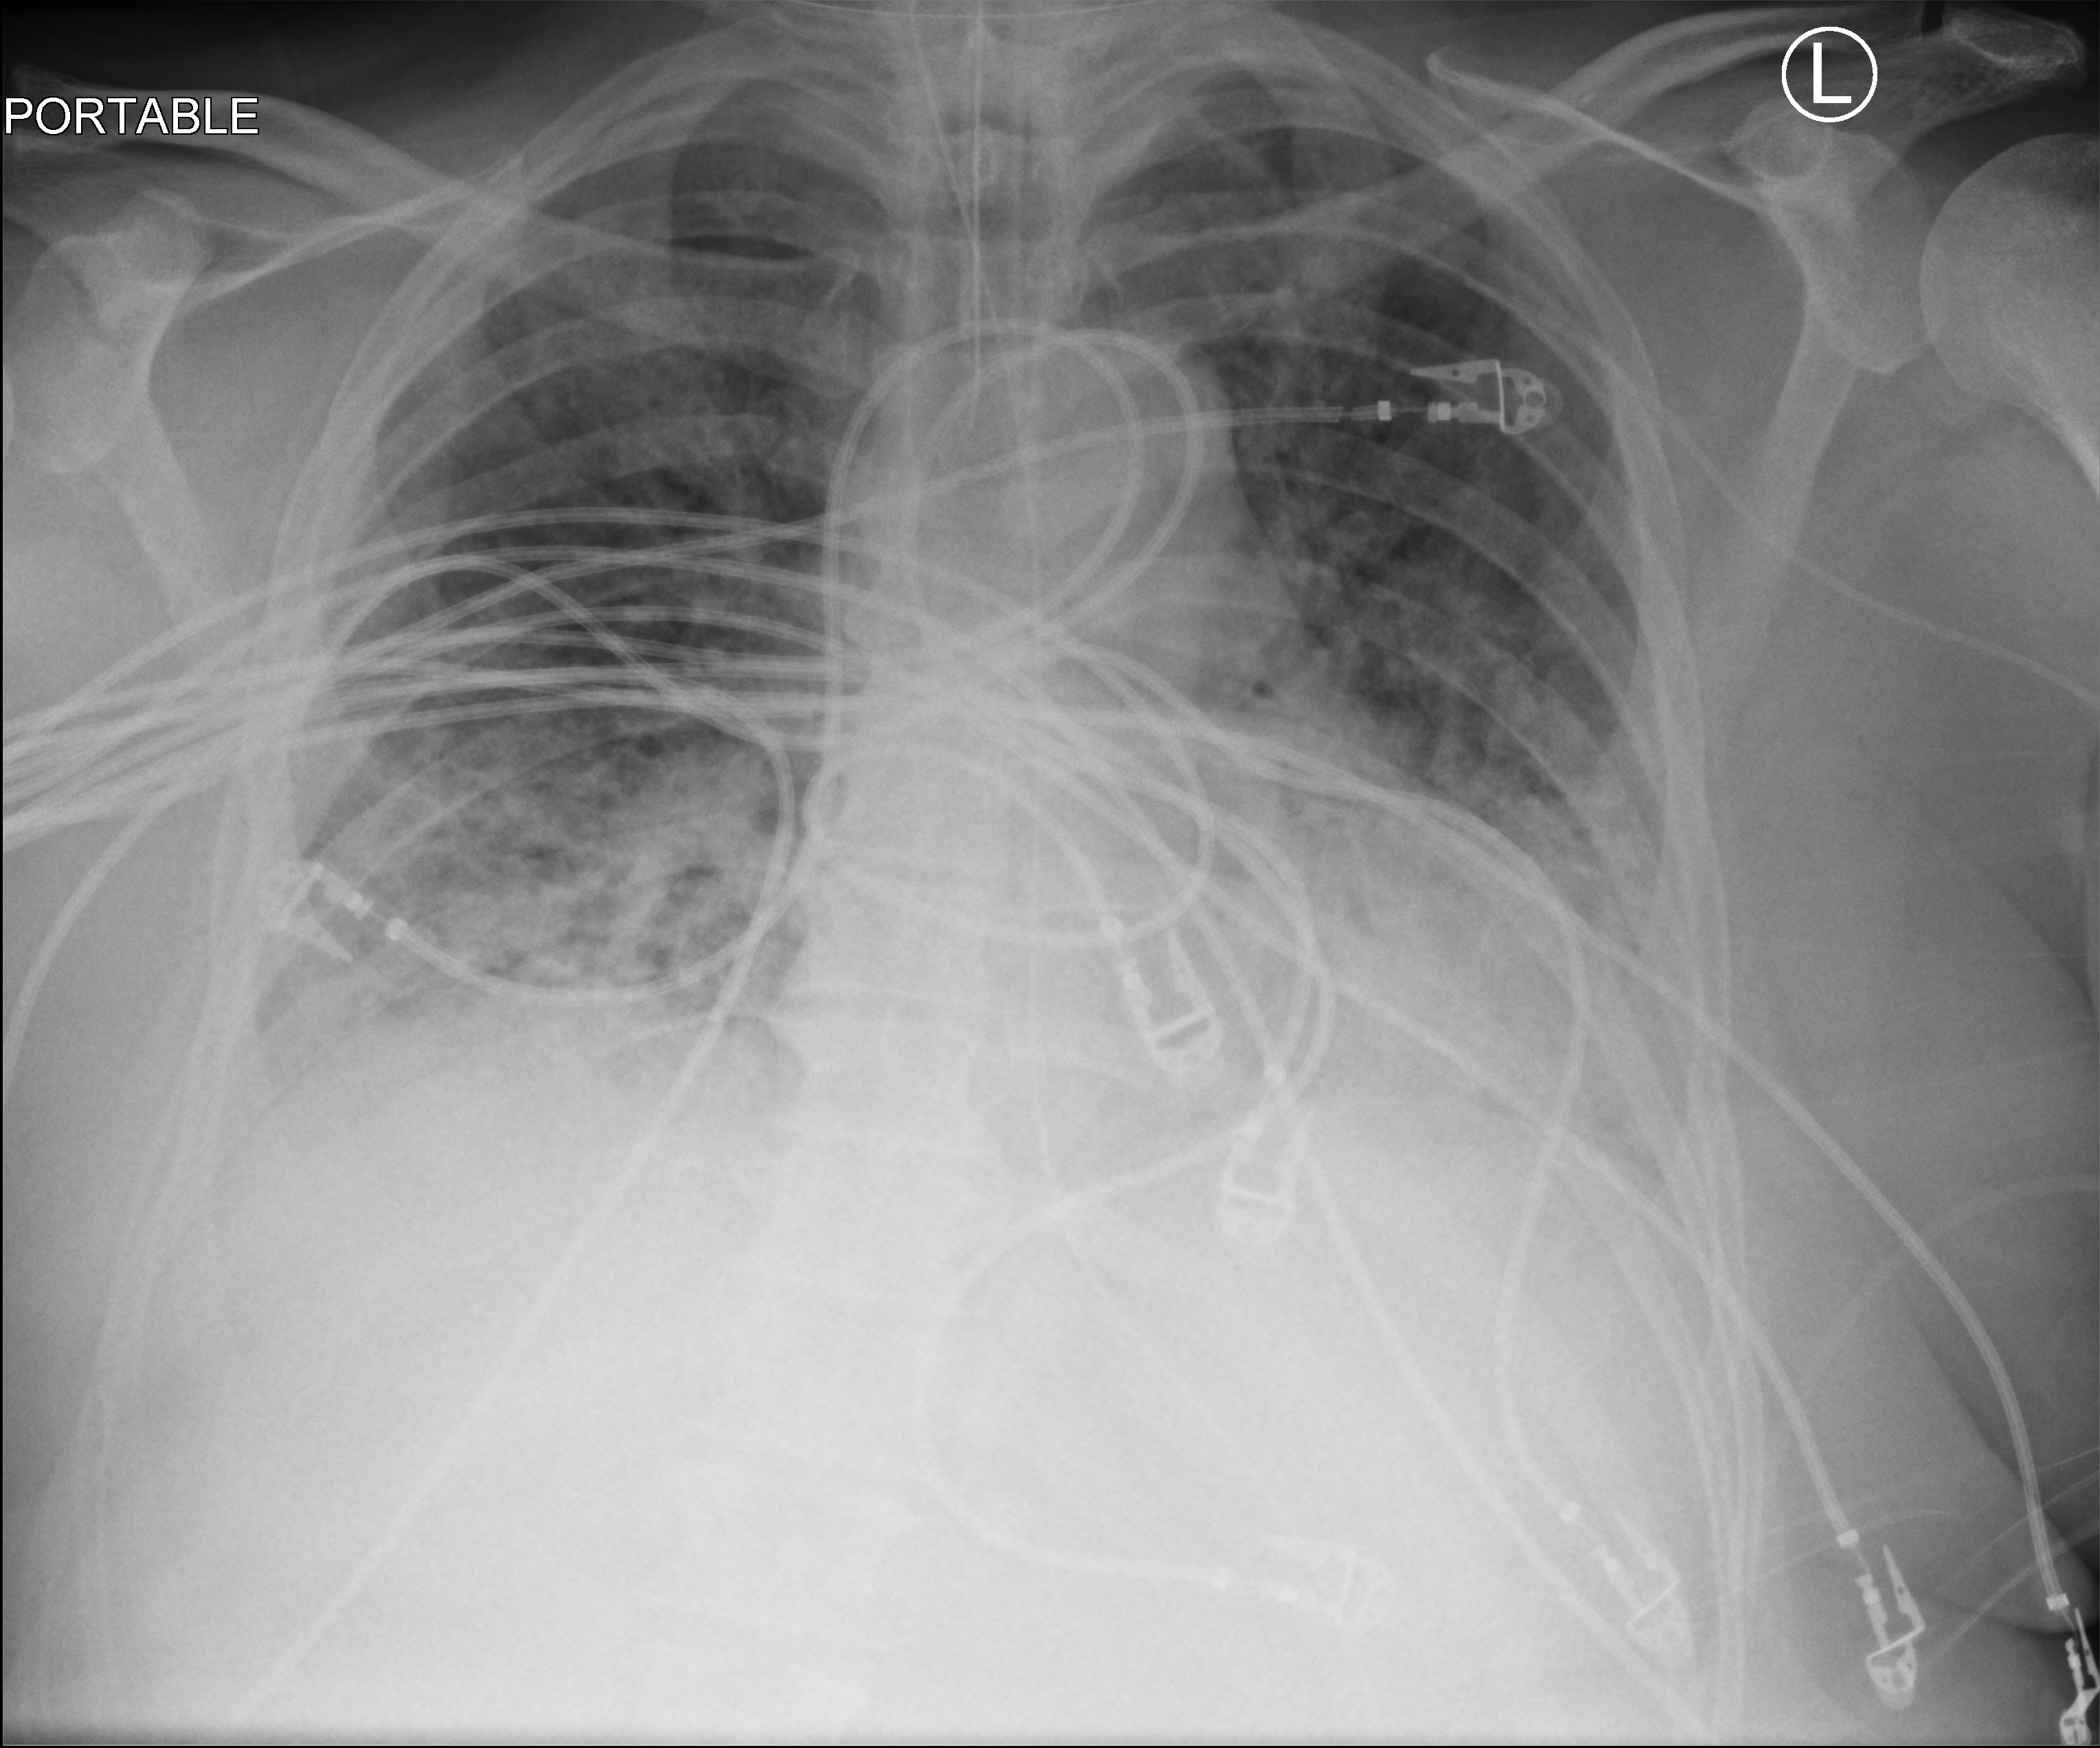
Bedside chest radiograph (computed radiography); anteroposterior (AP) projection. Patient hospitalised with COVID-19; male, aged 60–74 years.
From the hospital-stay record, not from the radiograph (when in the stay this image was taken is not recorded):
- mechanically ventilated during this hospital stay: yes